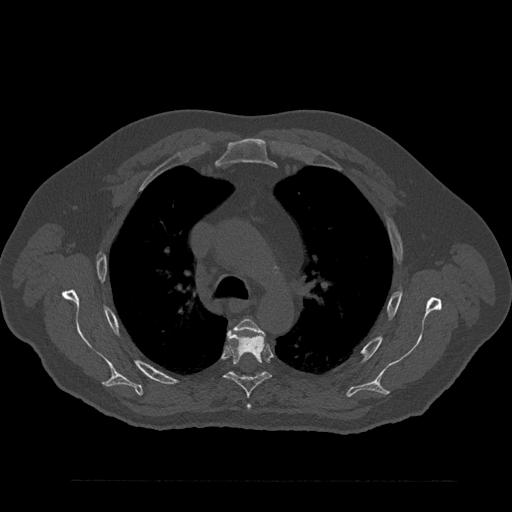
CT including the spine, one axial slice; position 605 of 797 along the scan axis; 120 kVp; bone window (W 1800 / L 400 HU); 512 × 512 image matrix. Male patient, age 61 years. Case-level facts recorded for this patient, not image findings: primary cancer: prostate.
Outlined on this slice (semi-automatic segmentation, software-assisted and operator-edited):
- T4 vertebra: bounding box <235,319,262,410> (left, top, right, bottom; pixels)
- T5 vertebra: <224,332,271,398>
- T6 vertebra: <232,373,264,377>